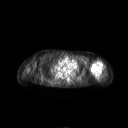
FDG PET of an extremity soft-tissue mass (from a PET/CT study), one axial slice. Slice 173 of 267 in the series (ordered by position). 3.27 mm slice thickness. 128 × 128 image matrix, field of view 700 × 700 mm. Female patient, age 83 years. From the clinical record (not read from this slice): histological type: pleiomorphic leiomyosarcoma; grade: high; site of the primary tumour: left biceps.
Annotated regions visible in this slice (expert contour drawn on MRI and transferred to this co-registered scan by the dataset authors):
- gross tumour volume including surrounding oedema: box from (x=90, y=59) to (x=103, y=77) px
- gross tumour volume (mass): (x=90, y=60)–(x=103, y=76)